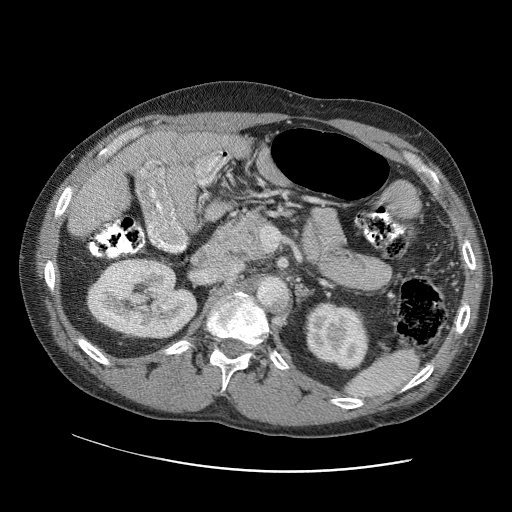
Contrast-enhanced abdominal CT (liver protocol), one axial slice. Position 49 of 109 along the scan axis. 120 kVp. Soft-tissue window (W 400 / L 40 HU). 512 × 512 image matrix. Case-level facts recorded for this patient, not image findings: diagnosis: hepatocellular carcinoma (patient treated with transarterial chemoembolisation; whether this scan precedes or follows treatment is not stated here); TNM stage (as recorded): Stage-IIIC.
Annotated regions visible in this slice (semi-automatic segmentation, software-assisted and operator-edited):
- liver parenchyma outside the tumour (the mass and vessels are separate outlines, so this box may not span the whole liver): box from (x=118, y=132) to (x=202, y=166) px
- liver vessels: (x=120, y=135)–(x=196, y=165)